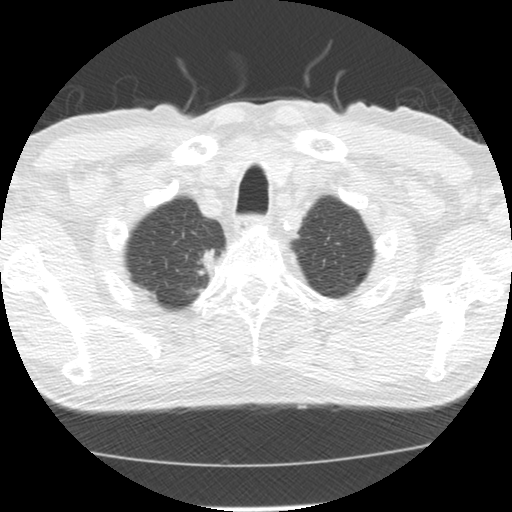
Low-dose screening chest CT, one axial slice; position 121 of 139 along the scan axis; 120 kVp; lung window (W 1500 / L -600 HU); 2.5 mm slice thickness; 512 × 512 image matrix, field of view 310 × 310 mm.
Structures marked on this image (outlined manually by an expert reader):
- lesion 1 (tumor, upper lobe of right lung): bounding box <197,248,218,279> (left, top, right, bottom; pixels)